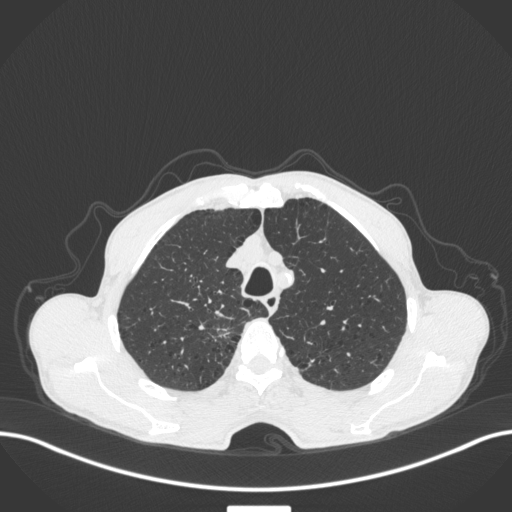
Chest CT, one axial slice; slice 340 of 445 in the series (ordered by position); 120 kVp; lung window (W 1500 / L -600 HU); 1 mm slice thickness; 512 × 512 image matrix, field of view 400 × 400 mm. Patient: male, 70 years. Case-level facts recorded for this patient, not image findings: clinical TNM (as recorded): T1a N0 M0; histopathological grade: G1-2.
Structures marked on this image (bounding box drawn by a radiologist):
- lung tumour (recorded histology: adenocarcinoma): bounding box [x1, y1, x2, y2] px = [211, 314, 240, 345]